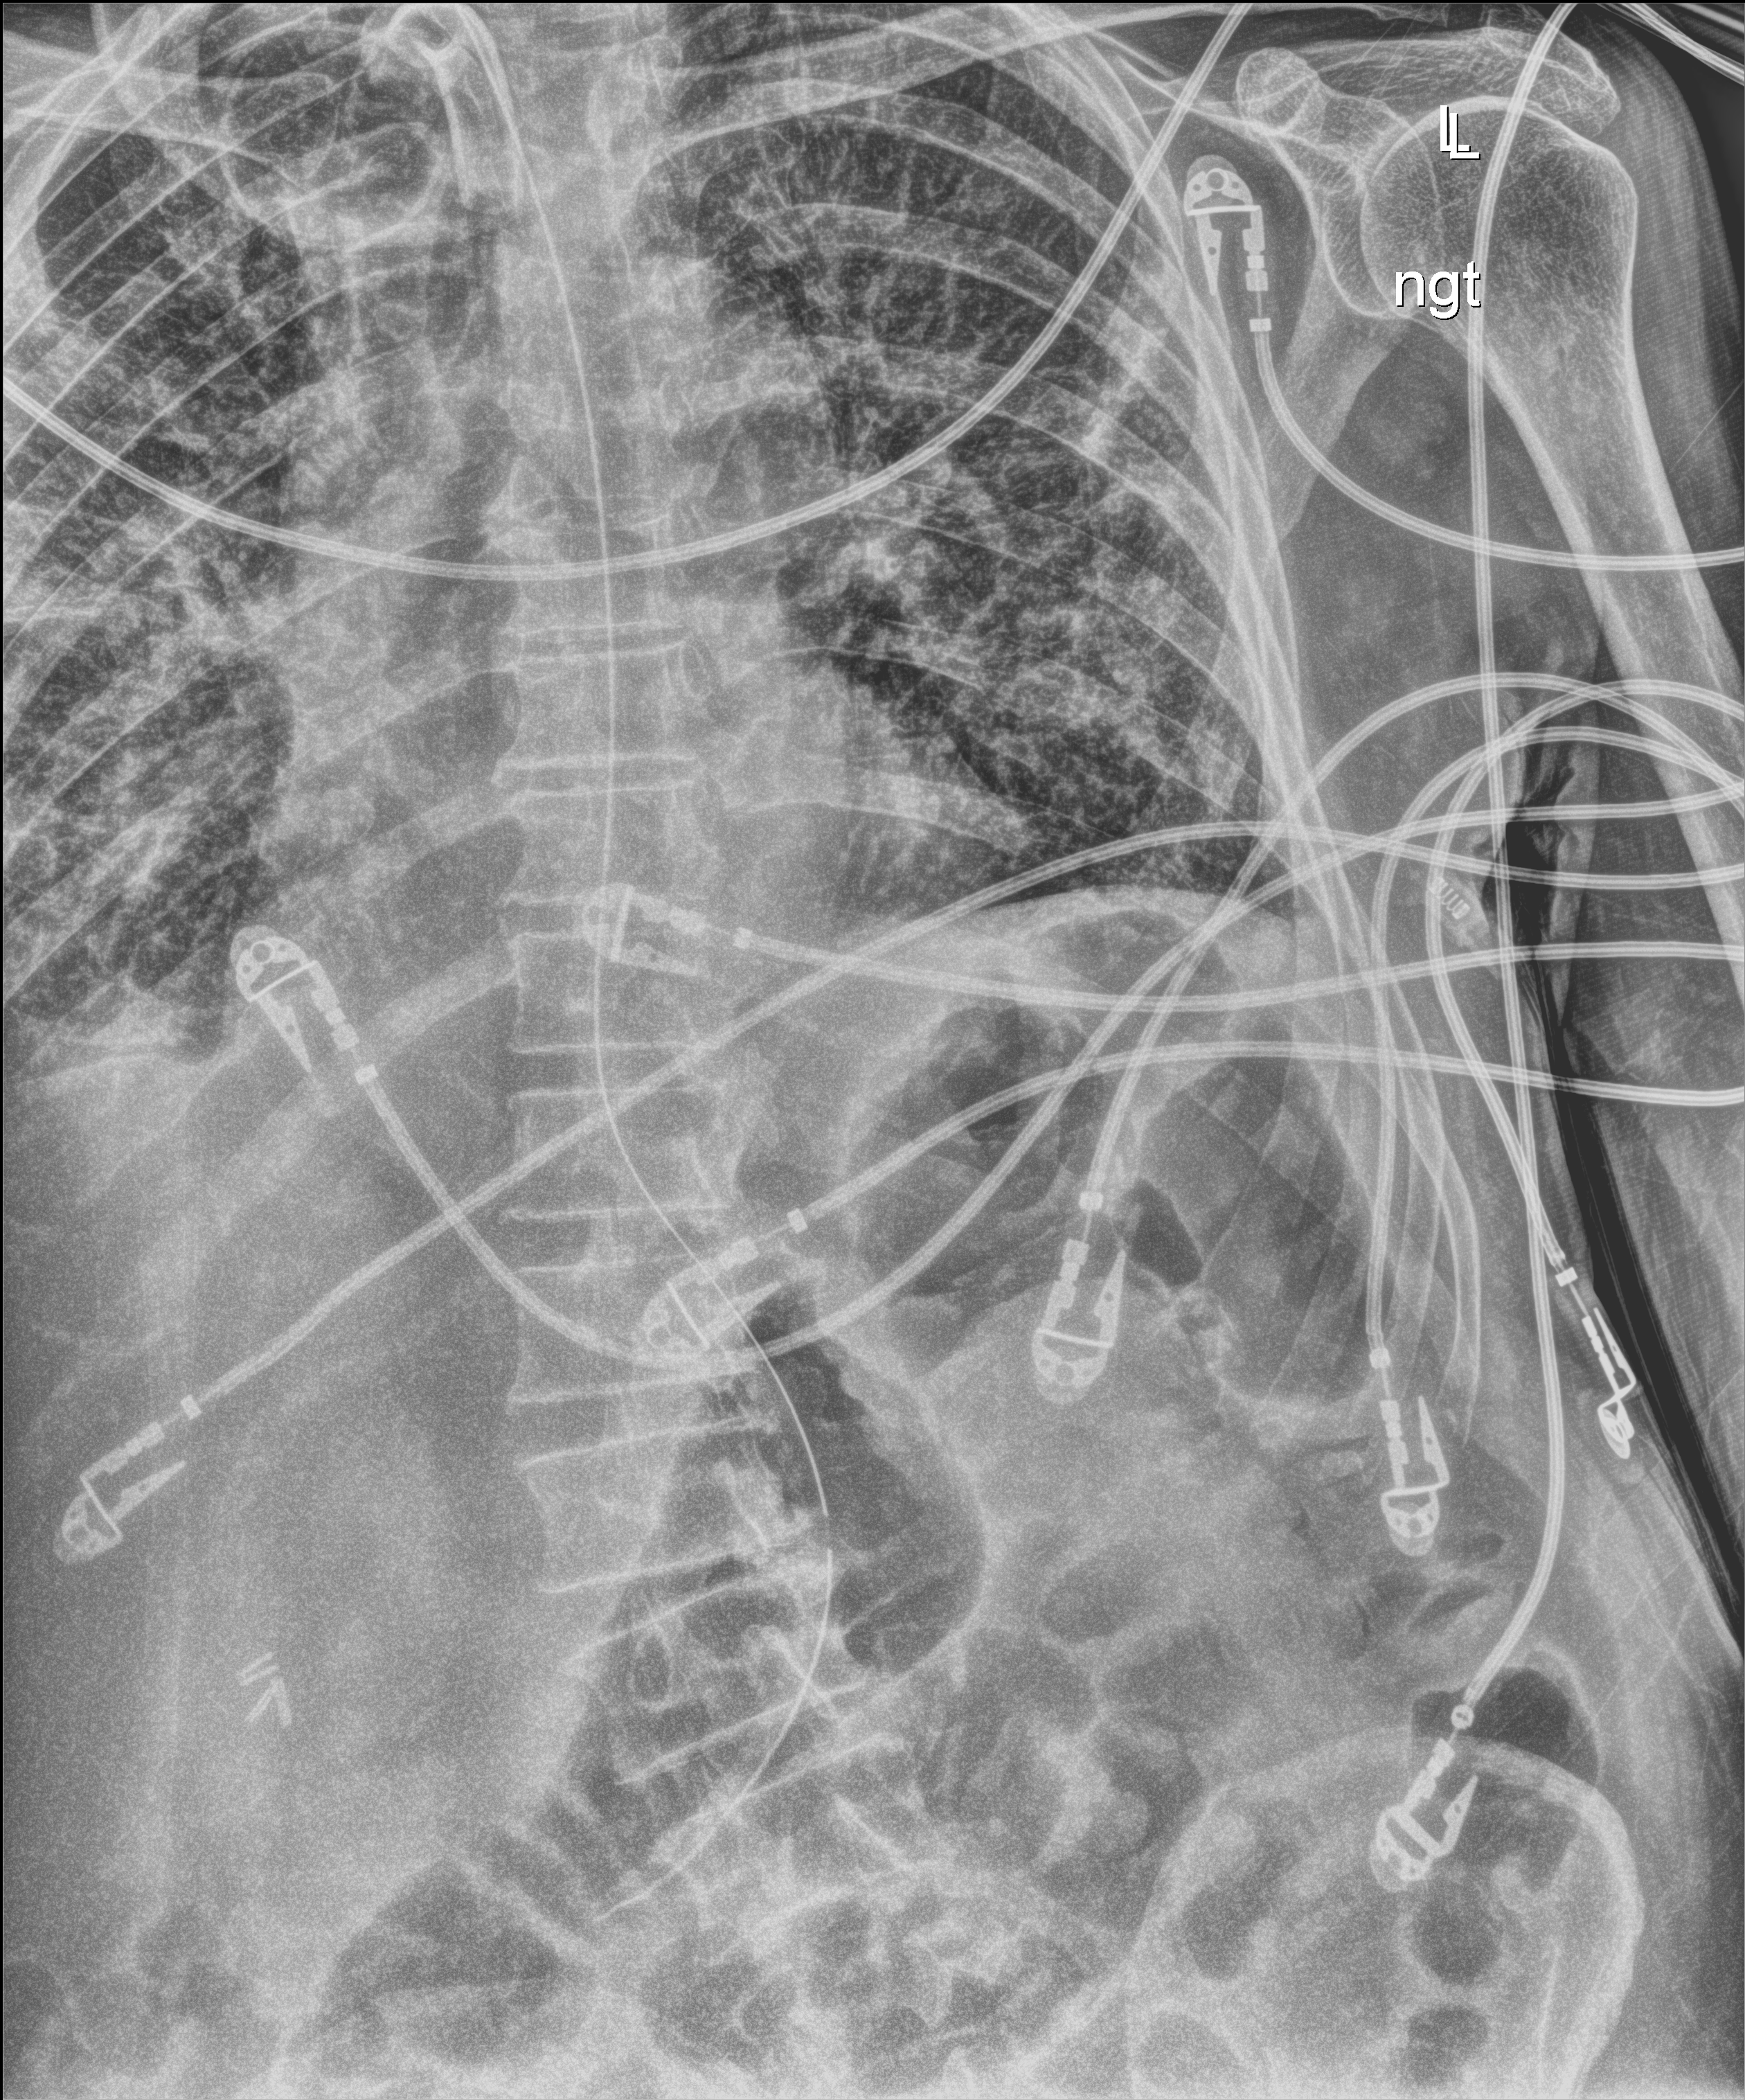
Bedside chest radiograph (digital radiography), anteroposterior (AP) projection. Male patient hospitalised with COVID-19, age 75–90 years.
Hospital-stay facts (about this admission, not read from this image; timing relative to this image not recorded): chronic kidney disease (admission record): no; mechanically ventilated during this hospital stay: yes.